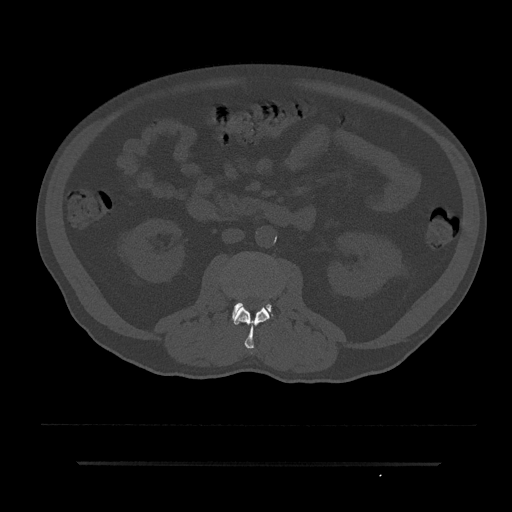
CT including the spine, one axial slice; position 43 of 797 along the scan axis; reconstruction kernel Br40s/3; 120 kVp; bone window (W 1800 / L 400 HU); 512 × 512 image matrix. Male patient, age 59 years. Case-level facts recorded for this patient, not image findings: primary cancer: bile ducts; vertebrae with lytic lesions (as recorded): T10.
Structures marked on this image (semi-automatic segmentation, software-assisted and operator-edited):
- L2 vertebra: bounding box (x1, y1, x2, y2) in pixels: (234, 305, 270, 355)
- L3 vertebra: (233, 302, 271, 317)